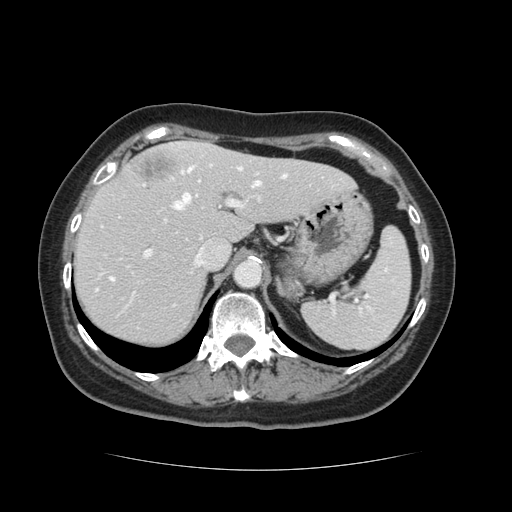
Contrast-enhanced abdominal CT, one axial slice; position 91 of 128 along the scan axis; 120 kVp; intravenous contrast given; soft-tissue window (W 400 / L 40 HU); 2.5 mm slice thickness; 512 × 512 image matrix, field of view 366 × 366 mm. Female patient, age 67 years. Case-level facts recorded for this patient, not image findings: diagnosis: colorectal cancer liver metastases, imaged before liver resection; multiple liver metastases: yes; largest metastasis: 3 cm.
Annotated regions visible in this slice (expert manual segmentation):
- hepatic veins: bounding box <111,167,287,280> (left, top, right, bottom; pixels)
- liver: <74,144,351,347>
- planned liver remnant (the part of the liver to remain after resection): <74,157,351,347>
- portal vein (with intrahepatic branches): <146,163,259,256>
- liver metastasis: <132,155,180,183>